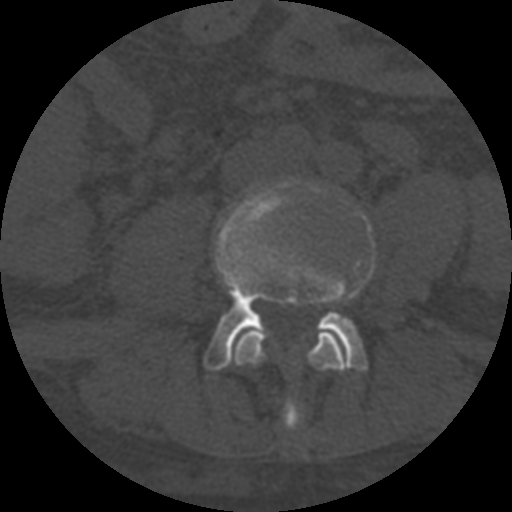
CT including the spine, one axial slice; position 218 of 708 along the scan axis; 120 kVp; one of 3 acquisitions stored at this slice position; bone window (W 1800 / L 400 HU); 1.25 mm slice thickness; 512 × 512 image matrix, field of view 160 × 160 mm. Patient age 55 years. From the clinical record (not read from this slice): primary cancer: colon.
Annotated regions visible in this slice (semi-automatically segmented with operator editing):
- L3 vertebra: box from (x=232, y=329) to (x=348, y=429) px
- L4 vertebra: (x=204, y=182)–(x=367, y=371)